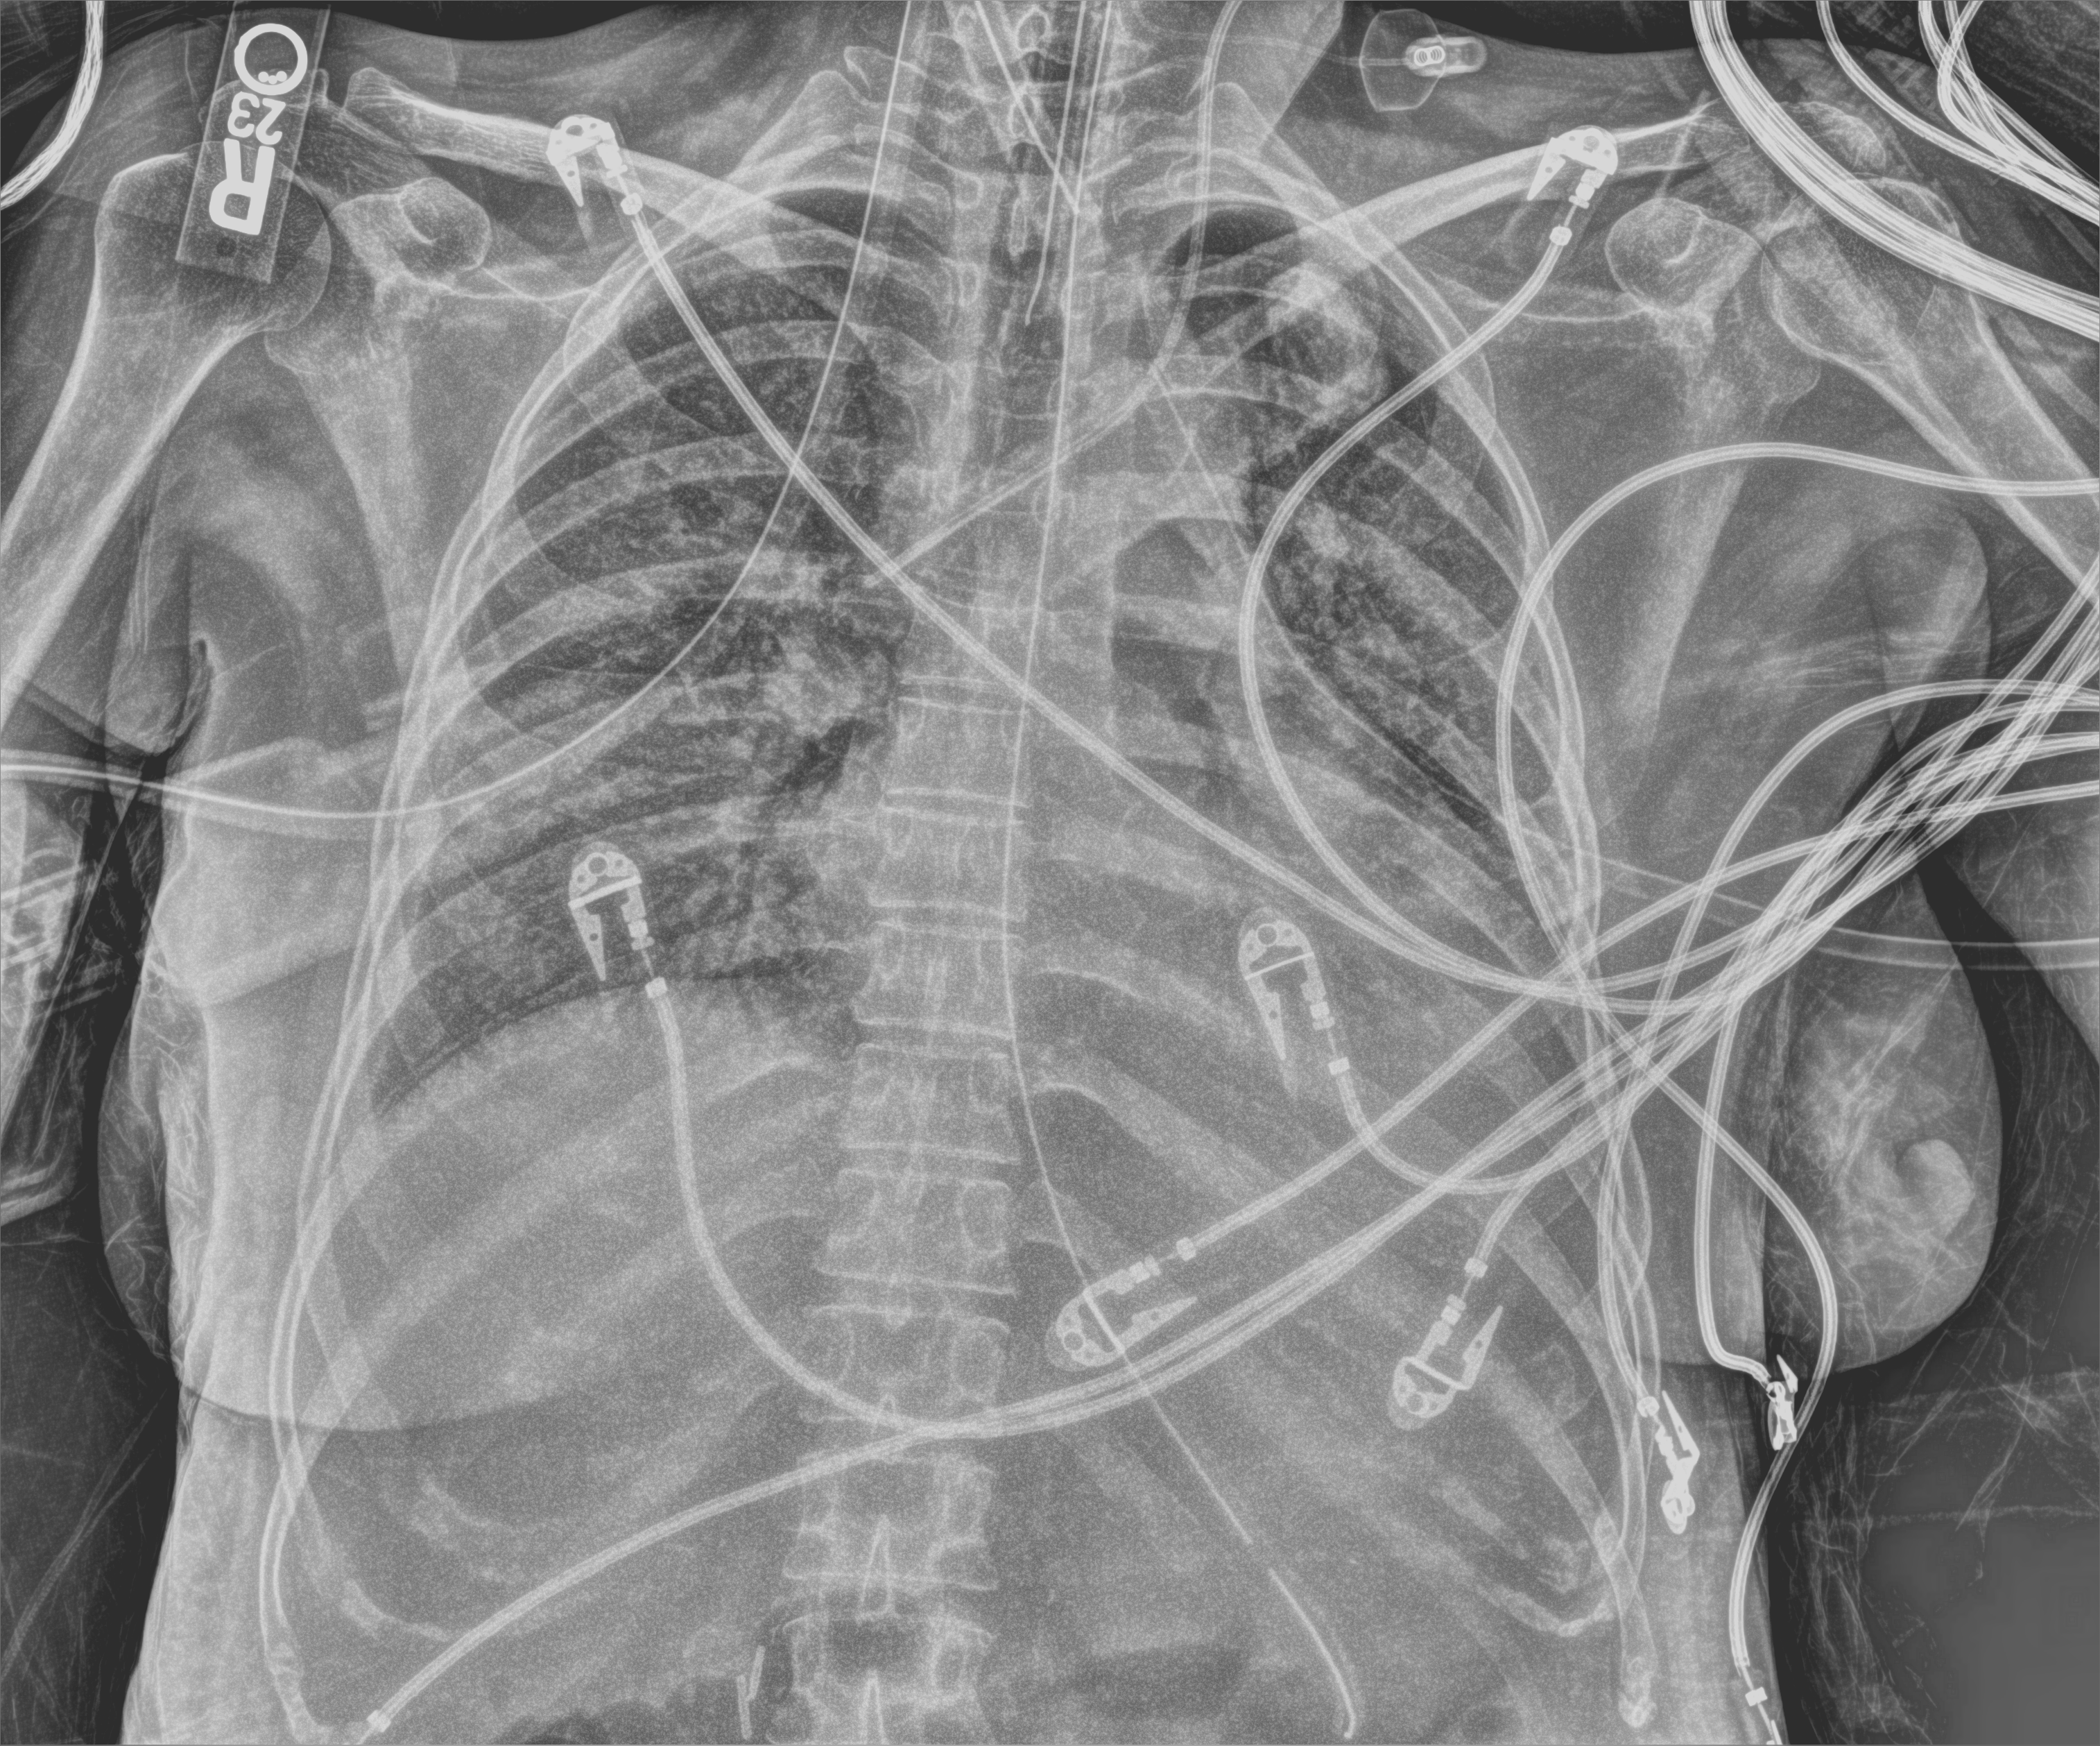
Chest X-ray (portable); anteroposterior (AP) projection. Patient hospitalised with COVID-19, aged 18–59 years.
Admission-level facts for this patient (not findings on this image; timing relative to this image not recorded):
- mechanically ventilated during this hospital stay: yes